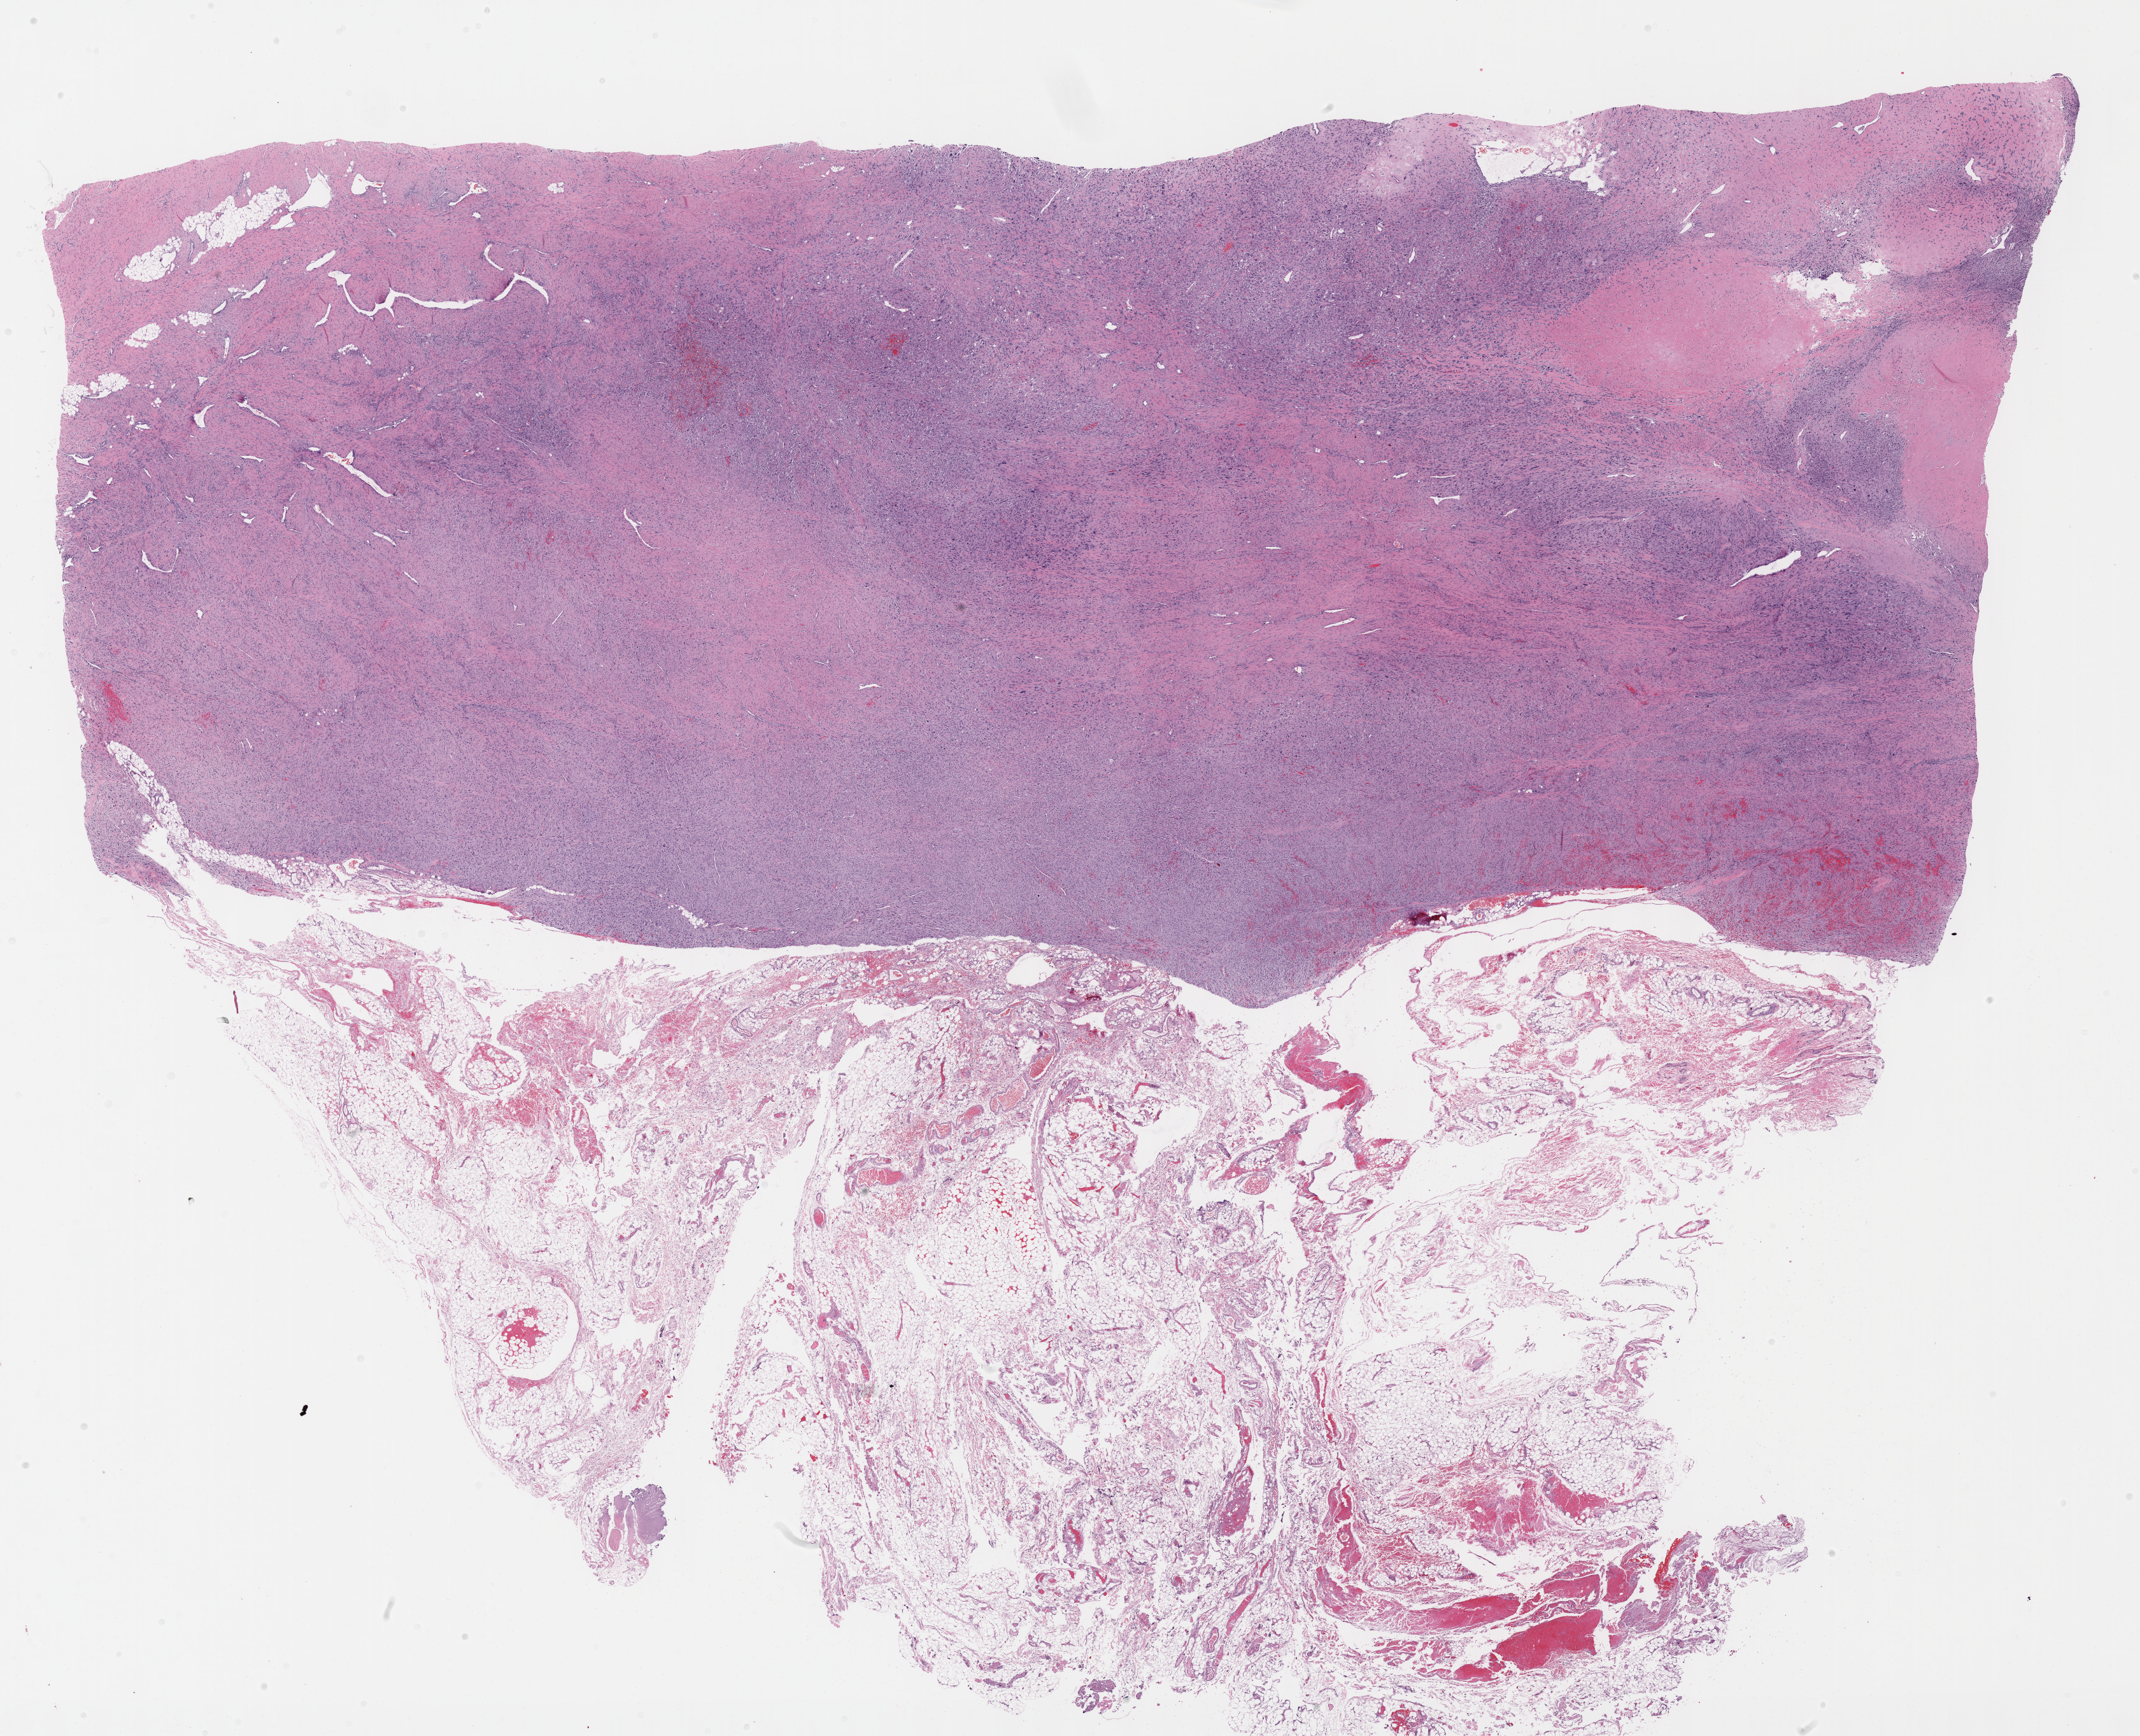
Digitized Hematoxylin and eosin (H&E) stained tissue section (whole slide) — a low-resolution overview of the entire scanned area, about 27.2 x 22.0 mm (acquisition: 40x scan), formalin-fixed paraffin-embedded (FFPE) diagnostic section, primary tumour sample from the connective, subcutaneous and other soft tissues. Male patient; age at initial diagnosis 76 years.
Histologic diagnosis: Malignant fibrous histiocytoma (connective, subcutaneous and other soft tissues of thorax).